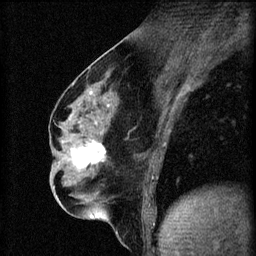
Breast MRI (dynamic contrast-enhanced), one sagittal slice; slice 30 of 60 in the series (ordered by position); 3 images stored at this slice position (order not interpretable as contrast timing); 1.5 T; TE 4.2 ms, TR 8.2 ms; 2 mm slice thickness; 256 × 256 image matrix. Patient: female, 56 years.
Structures marked on this image (semi-automatic segmentation, software-assisted and operator-edited):
- analysis volume of interest (the breast-tissue region the enhancement analysis was run in; not a lesion): bounding box [x1, y1, x2, y2] px = [62, 136, 109, 179]
- tumour enhancement mask (voxels above the 70 % enhancement threshold inside the analysis volume of interest): [62, 140, 105, 169]